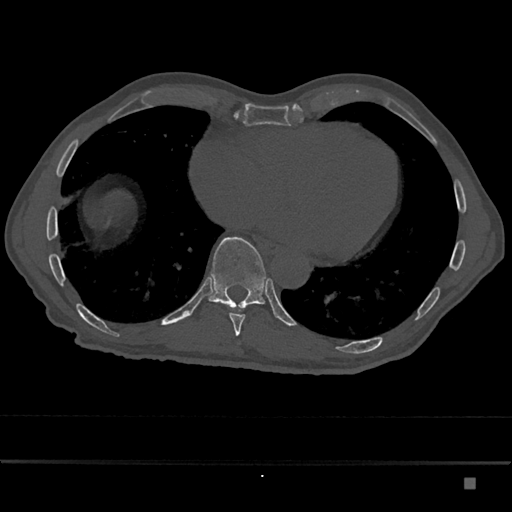
CT including the spine, one axial slice; reconstruction kernel Br40s/3; bone window (W 1800 / L 400 HU); 0.5 mm slice thickness; 512 × 512 image matrix. Patient: male, 72 years. Case-level facts recorded for this patient, not image findings: primary cancer: prostate.
Outlined on this slice (semi-automatically segmented with operator editing):
- T10 vertebra: box from (x=208, y=237) to (x=266, y=310) px
- T9 vertebra: (x=229, y=305)–(x=247, y=336)